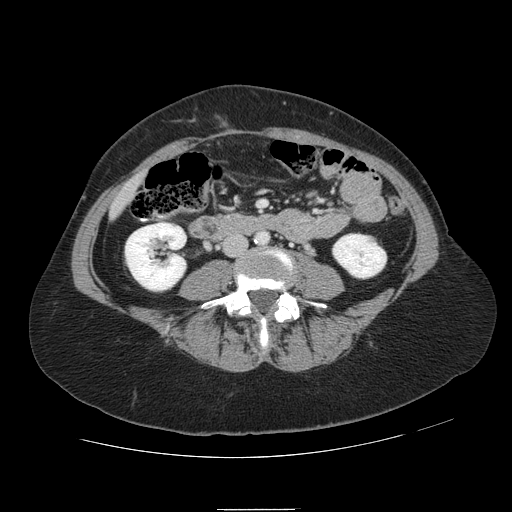
Contrast-enhanced abdominal CT, one axial slice; slice 1 of 121 in the series (ordered by position); 120 kVp; intravenous contrast given; soft-tissue window (W 400 / L 40 HU); 2.5 mm slice thickness; 512 × 512 image matrix, field of view 400 × 400 mm. Female patient, age 52 years. Case-level facts recorded for this patient, not image findings: diagnosis: colorectal cancer liver metastases, imaged before liver resection.
Outlined on this slice (expert manual segmentation):
- liver: box from (x=112, y=174) to (x=144, y=215) px